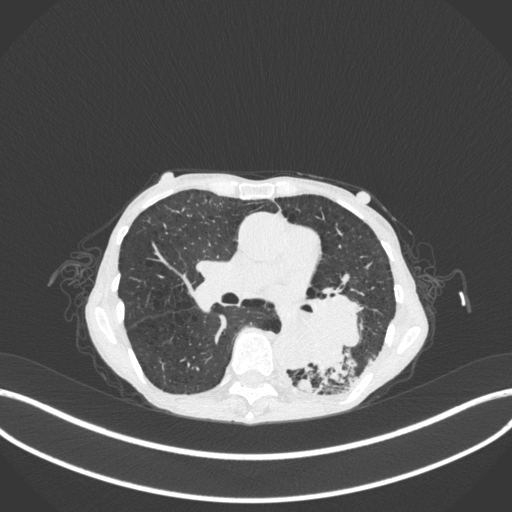
Chest CT, one axial slice. Slice 144 of 347 in the series (ordered by position). Reconstruction kernel B31f. 120 kVp. Lung window (W 1500 / L -600 HU). 512 × 512 image matrix, field of view 400 × 400 mm. Female patient, age 70 years. Case-level facts recorded for this patient, not image findings: clinical TNM (as recorded): T3 N0 M0.
Structures marked on this image (bounding box drawn by a radiologist):
- lung tumour (recorded histology: small cell carcinoma): bounding box <287,281,377,381> (left, top, right, bottom; pixels)